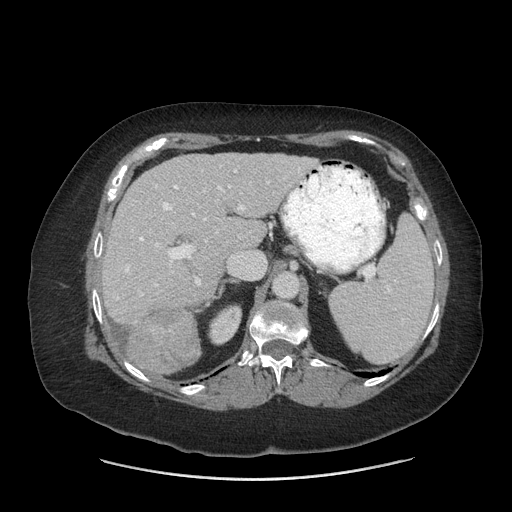
Contrast-enhanced abdominal CT (liver protocol), one axial slice. Slice 43 of 69 in the series (ordered by position). Soft-tissue window (W 400 / L 40 HU). 512 × 512 image matrix. Case-level facts recorded for this patient, not image findings: diagnosis: hepatocellular carcinoma (patient treated with transarterial chemoembolisation; whether this scan precedes or follows treatment is not stated here); TNM stage (as recorded): Stage-IIIB; Child-Pugh class: A; tumour differentiation: moderately differentiated; tumour nodularity: multinodular.
Annotated regions visible in this slice (semi-automatic segmentation, software-assisted and operator-edited):
- liver parenchyma outside the tumour (the mass and vessels are separate outlines, so this box may not span the whole liver): box from (x=102, y=152) to (x=316, y=348) px
- mass: (x=127, y=302)–(x=201, y=373)
- liver vessels: (x=116, y=168)–(x=301, y=300)